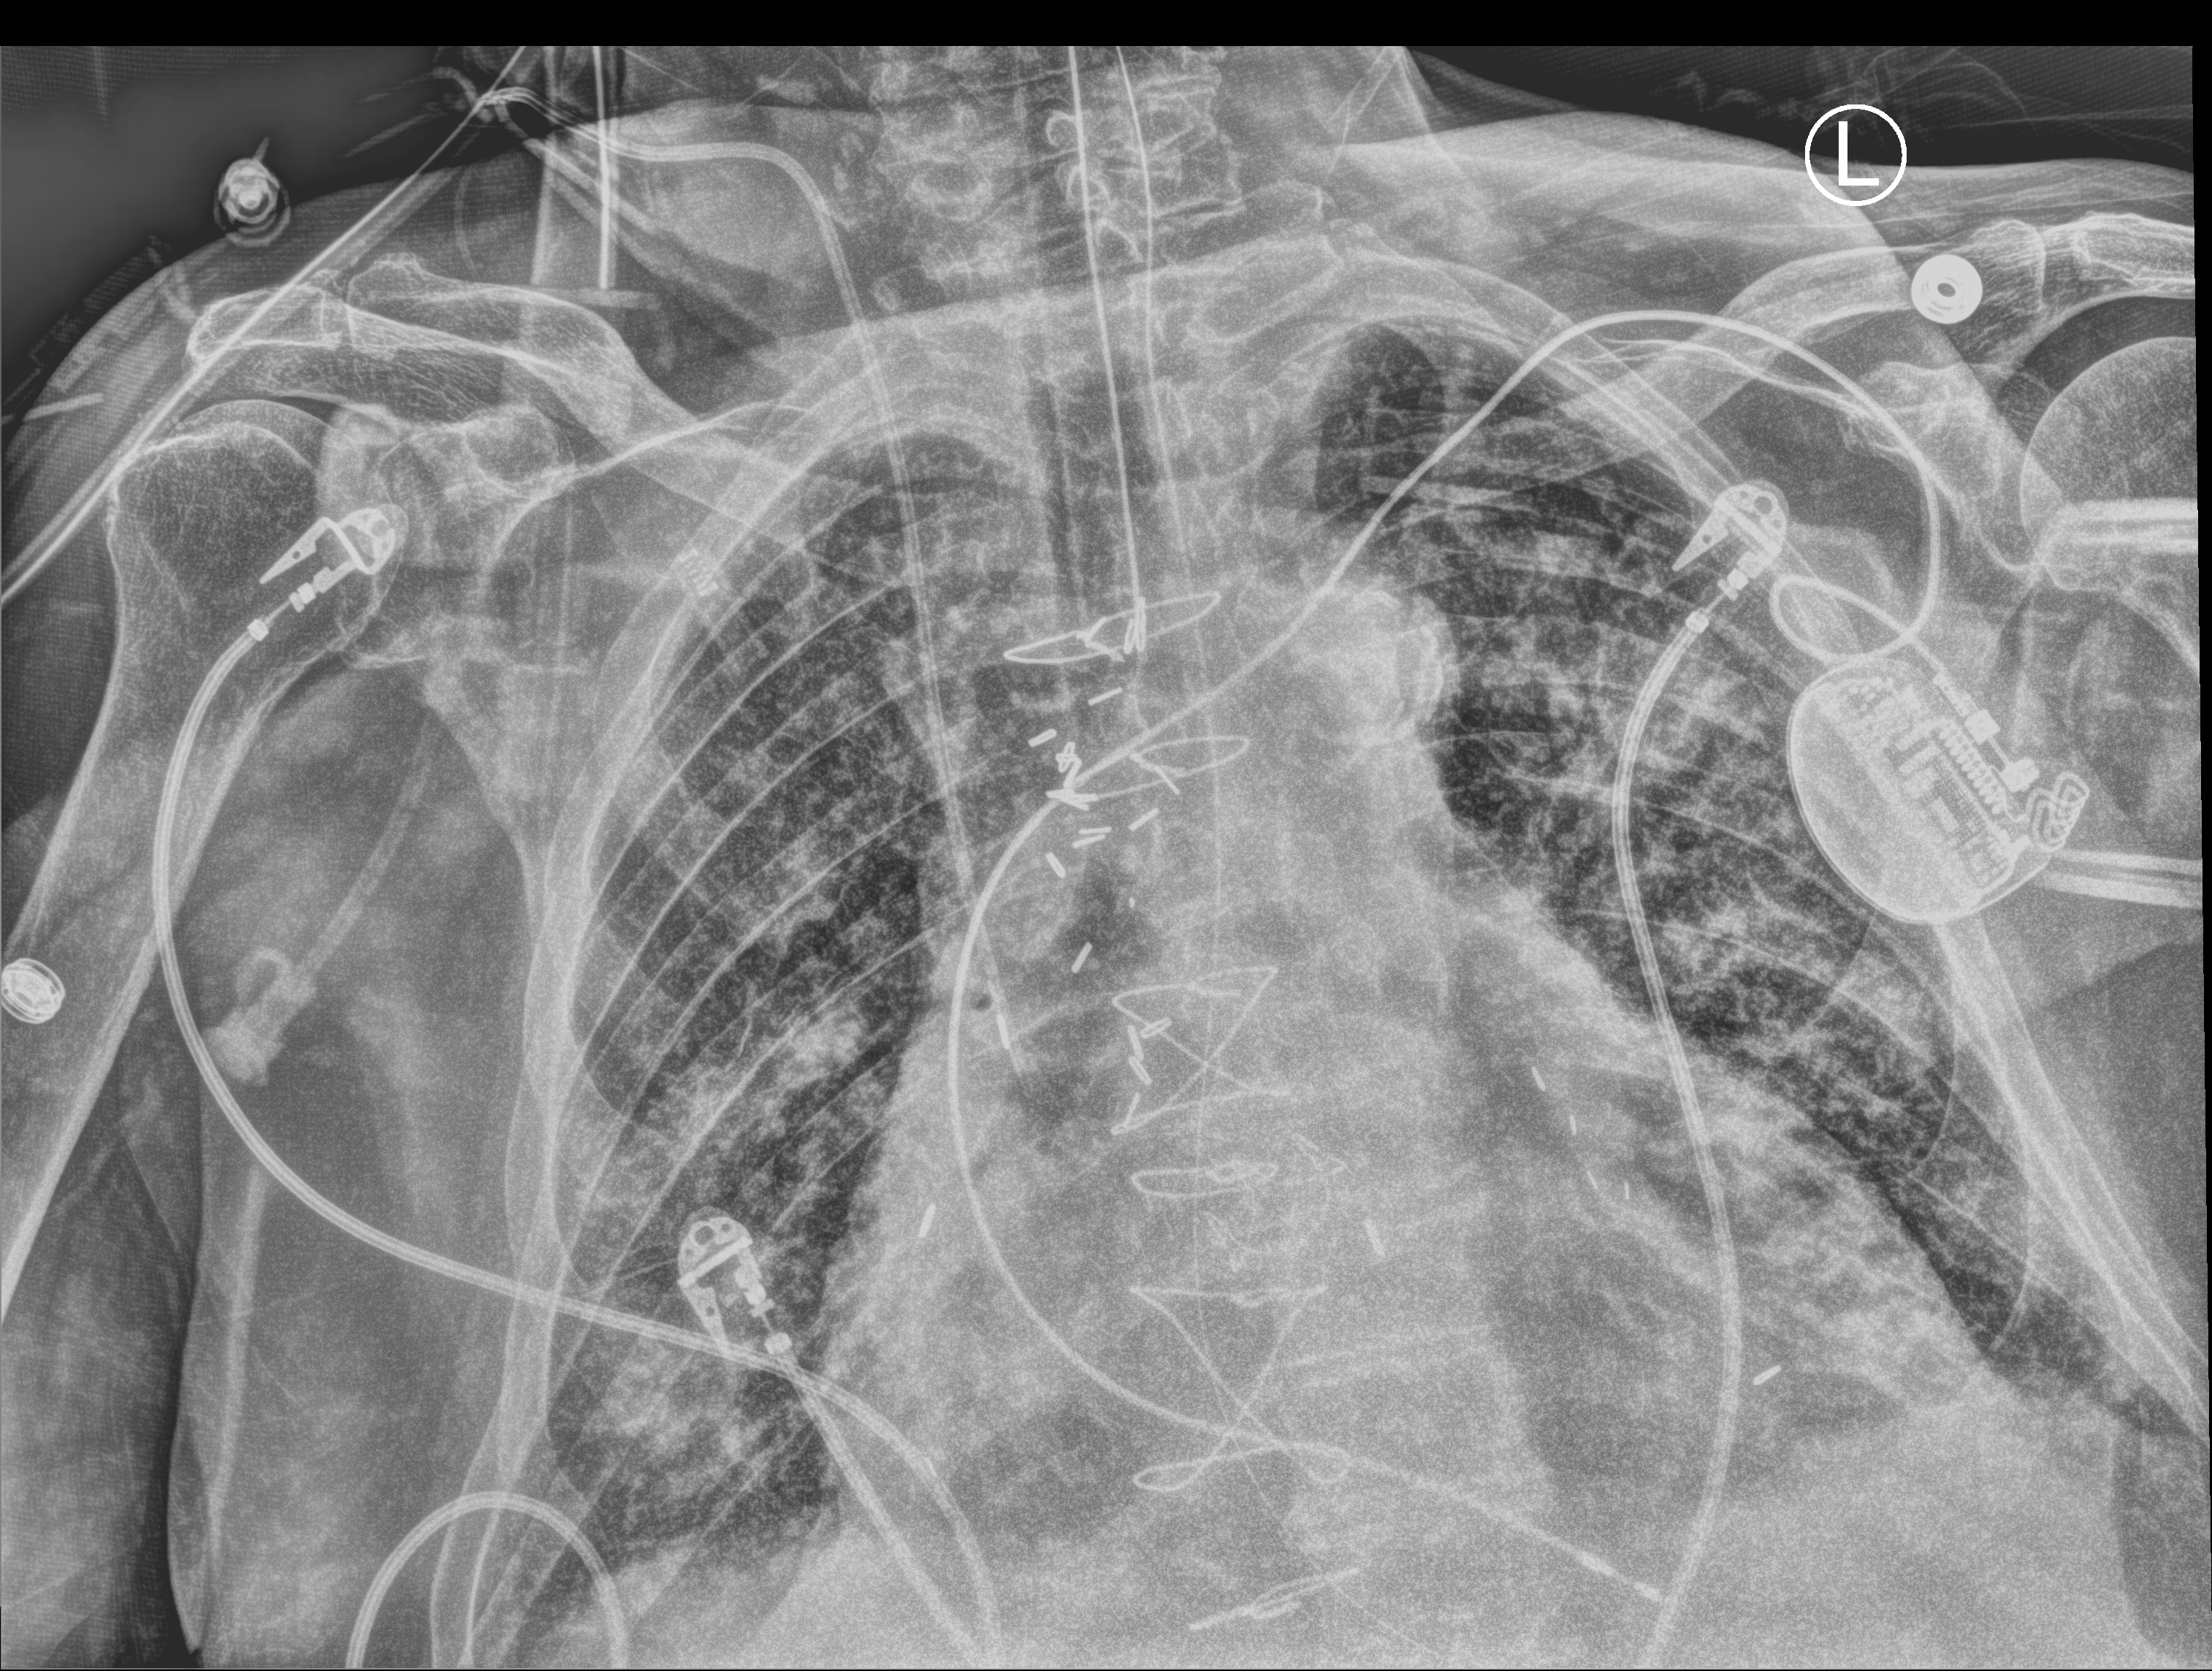
Chest X-ray (portable). Male patient hospitalised with COVID-19, age 75–90 years.
From the hospital-stay record, not from the radiograph (when in the stay this image was taken is not recorded): admitted to intensive care during this hospital stay: yes.